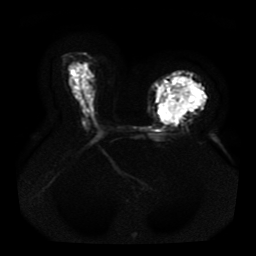
Breast MRI, one axial slice; slice 25 of 41 in the series (ordered by position); diffusion-weighted series; image 2 of 4 stored at this slice position (different b-values; order by instance number); 1.5 T; 5 mm slice thickness; 256 × 256 image matrix. Female patient.
Annotated regions visible in this slice (outlined manually by an expert reader):
- tumour on diffusion-weighted imaging: bounding box (x1, y1, x2, y2) in pixels: (156, 78, 205, 124)